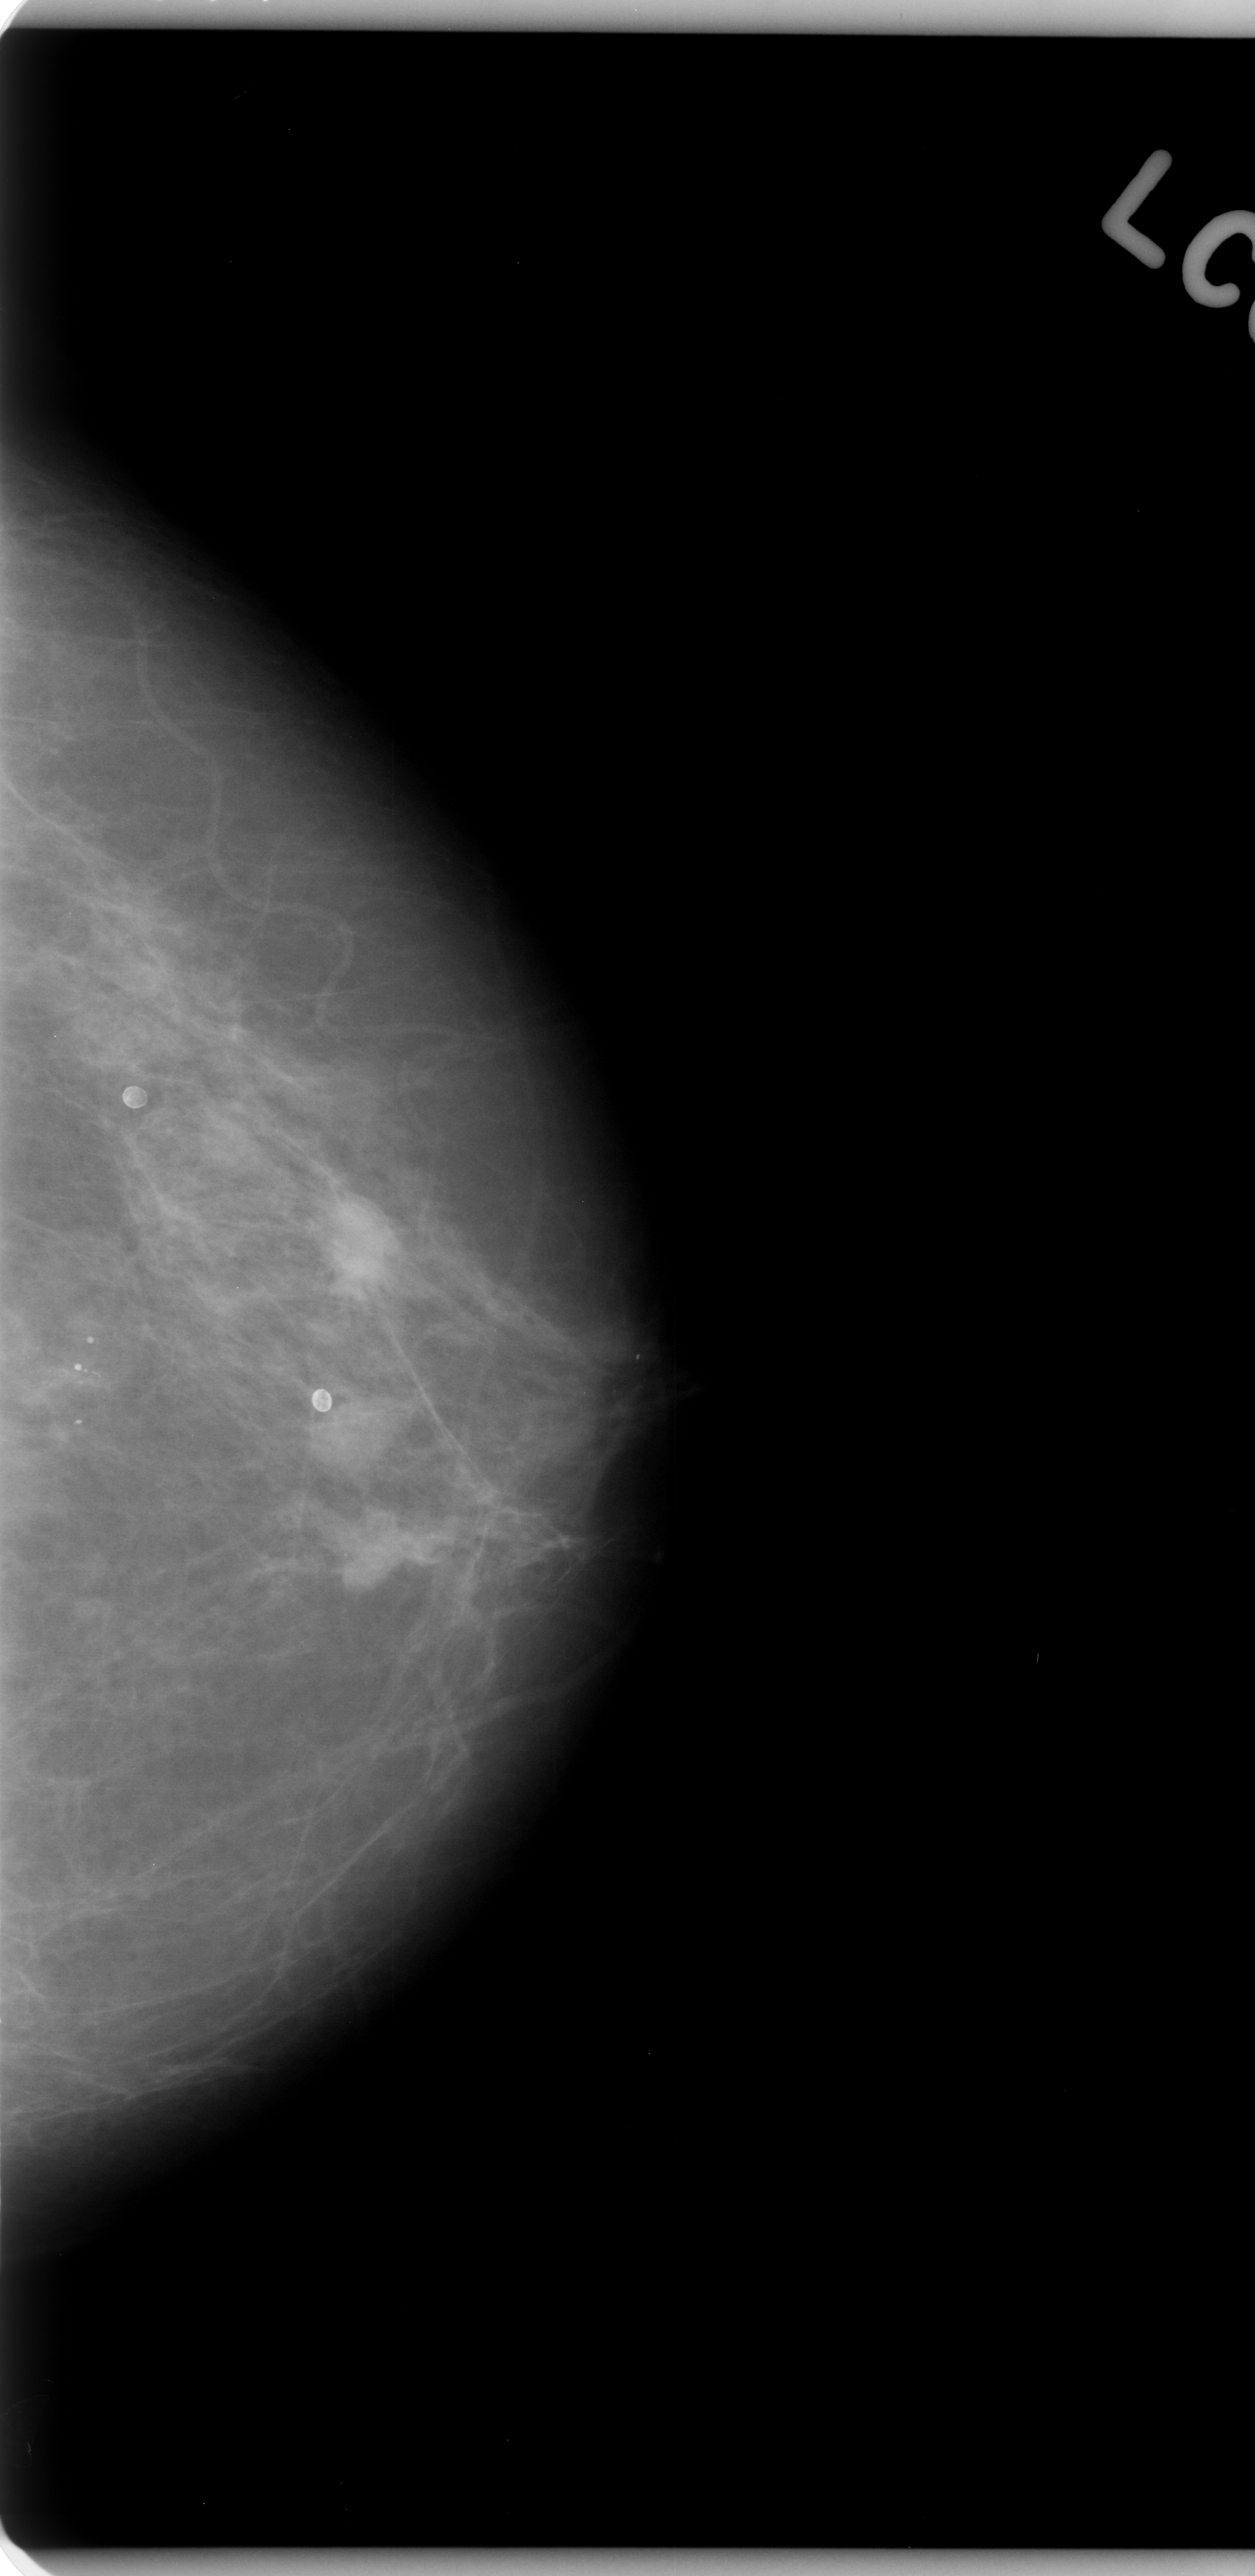
Scanned film-screen mammogram; left breast; craniocaudal (CC) view; BI-RADS breast density category 1 (scale 1–4); 1255 × 2576 image matrix.
Expert-marked regions of interest on this film, with their recorded descriptors:
- Finding 1 of 3: mass, shape oval, margins microlobulated; BI-RADS assessment category 4; pathology (as recorded): malignant: bounding box <261,1356,389,1465> (left, top, right, bottom; pixels)
- Finding 2 of 3: mass, shape oval, margins microlobulated; BI-RADS assessment category 4; pathology (as recorded): malignant: <308,1186,405,1302>
- Finding 3 of 3: mass, shape oval, margins microlobulated; BI-RADS assessment category 4; pathology (as recorded): malignant: <334,1514,436,1593>